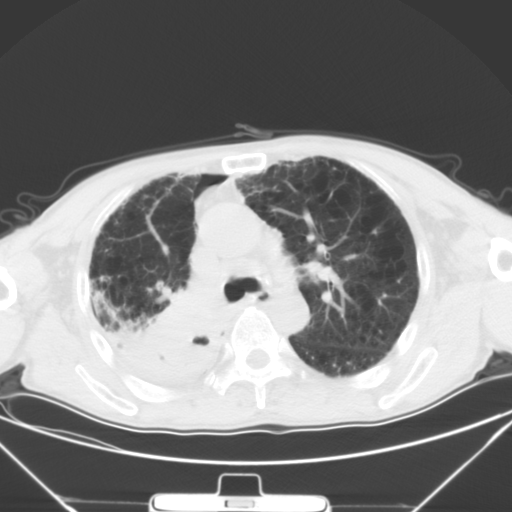
Chest CT, one axial slice. Position 32 of 50 along the scan axis. Lung window (W 1500 / L -600 HU). 5 mm slice thickness. 512 × 512 image matrix. Male patient, age 65 years. From the clinical record (not read from this slice): clinical TNM (as recorded): T3 N1 M1a.
Annotated regions visible in this slice (bounding box drawn by a radiologist):
- lung tumour (recorded histology: squamous cell carcinoma): bounding box (x1, y1, x2, y2) in pixels: (141, 295, 220, 380)